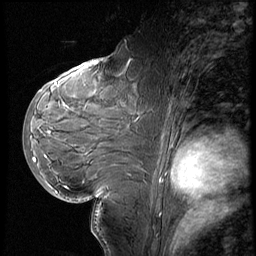
Breast MRI (dynamic contrast-enhanced), one sagittal slice. Slice 33 of 60 in the series (ordered by position). 3 images stored at this slice position (order not interpretable as contrast timing). 1.5 T. TE 4.2 ms, TR 8.9 ms. 2.5 mm slice thickness. 256 × 256 image matrix, field of view 200 × 200 mm. Female patient, age 29 years. From the clinical record (not read from this slice): setting: breast cancer imaged before/during neoadjuvant chemotherapy.
Annotated regions visible in this slice (semi-automatic segmentation, software-assisted and operator-edited):
- analysis volume of interest (the breast-tissue region the enhancement analysis was run in; not a lesion): bounding box (x1, y1, x2, y2) in pixels: (29, 57, 151, 200)
- tumour enhancement mask (voxels above the 140 % enhancement threshold inside the analysis volume of interest): (35, 83, 58, 161)